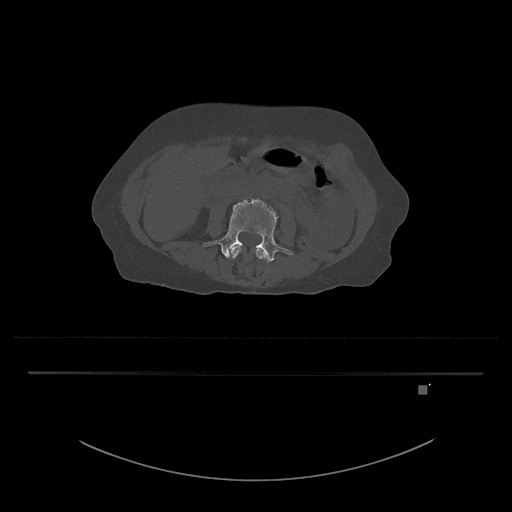
CT including the spine, one axial slice. Reconstruction kernel Br40s/3. Bone window (W 1800 / L 400 HU). 512 × 512 image matrix, field of view 500 × 500 mm. Female patient, age 57 years. Case-level facts recorded for this patient, not image findings: primary cancer: cervical.
Annotated regions visible in this slice (semi-automatic segmentation, software-assisted and operator-edited):
- L3 vertebra: box from (x=230, y=245) to (x=267, y=260) px
- L4 vertebra: (x=203, y=198)–(x=294, y=263)